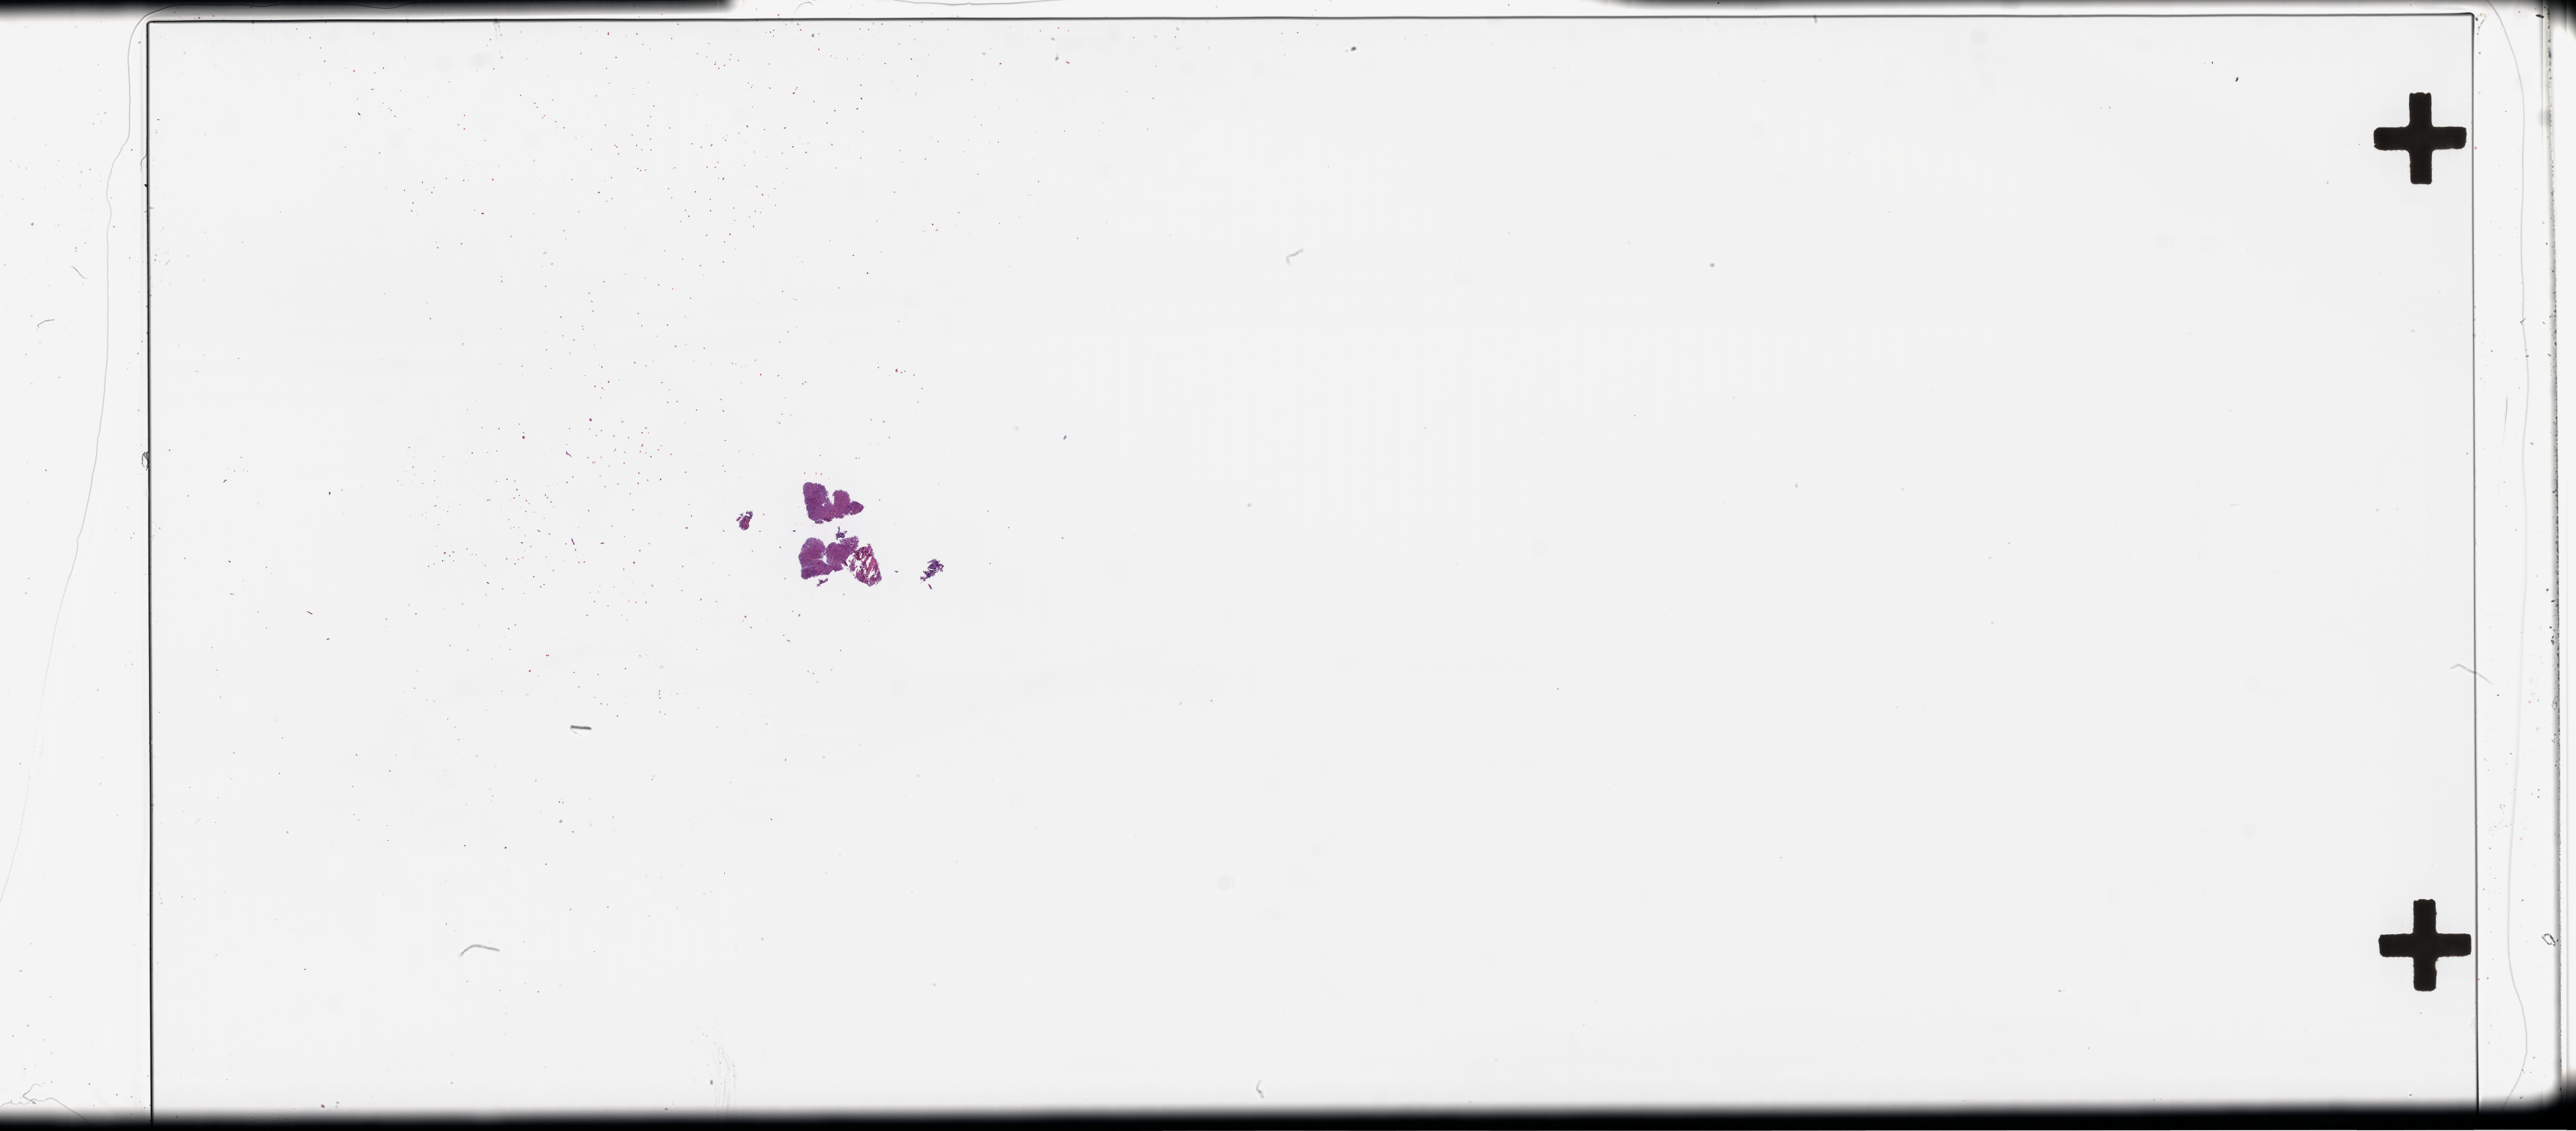
Digitized haematoxylin and eosin-stained section, a low-resolution overview of the entire scanned area, about 55.8 x 24.5 mm, FFPE section, collected at baseline (before treatment). Female patient.
This section: metastasis (sampled organ not recorded). Primary diagnosis of the patient: Colorectal Carcinoma.